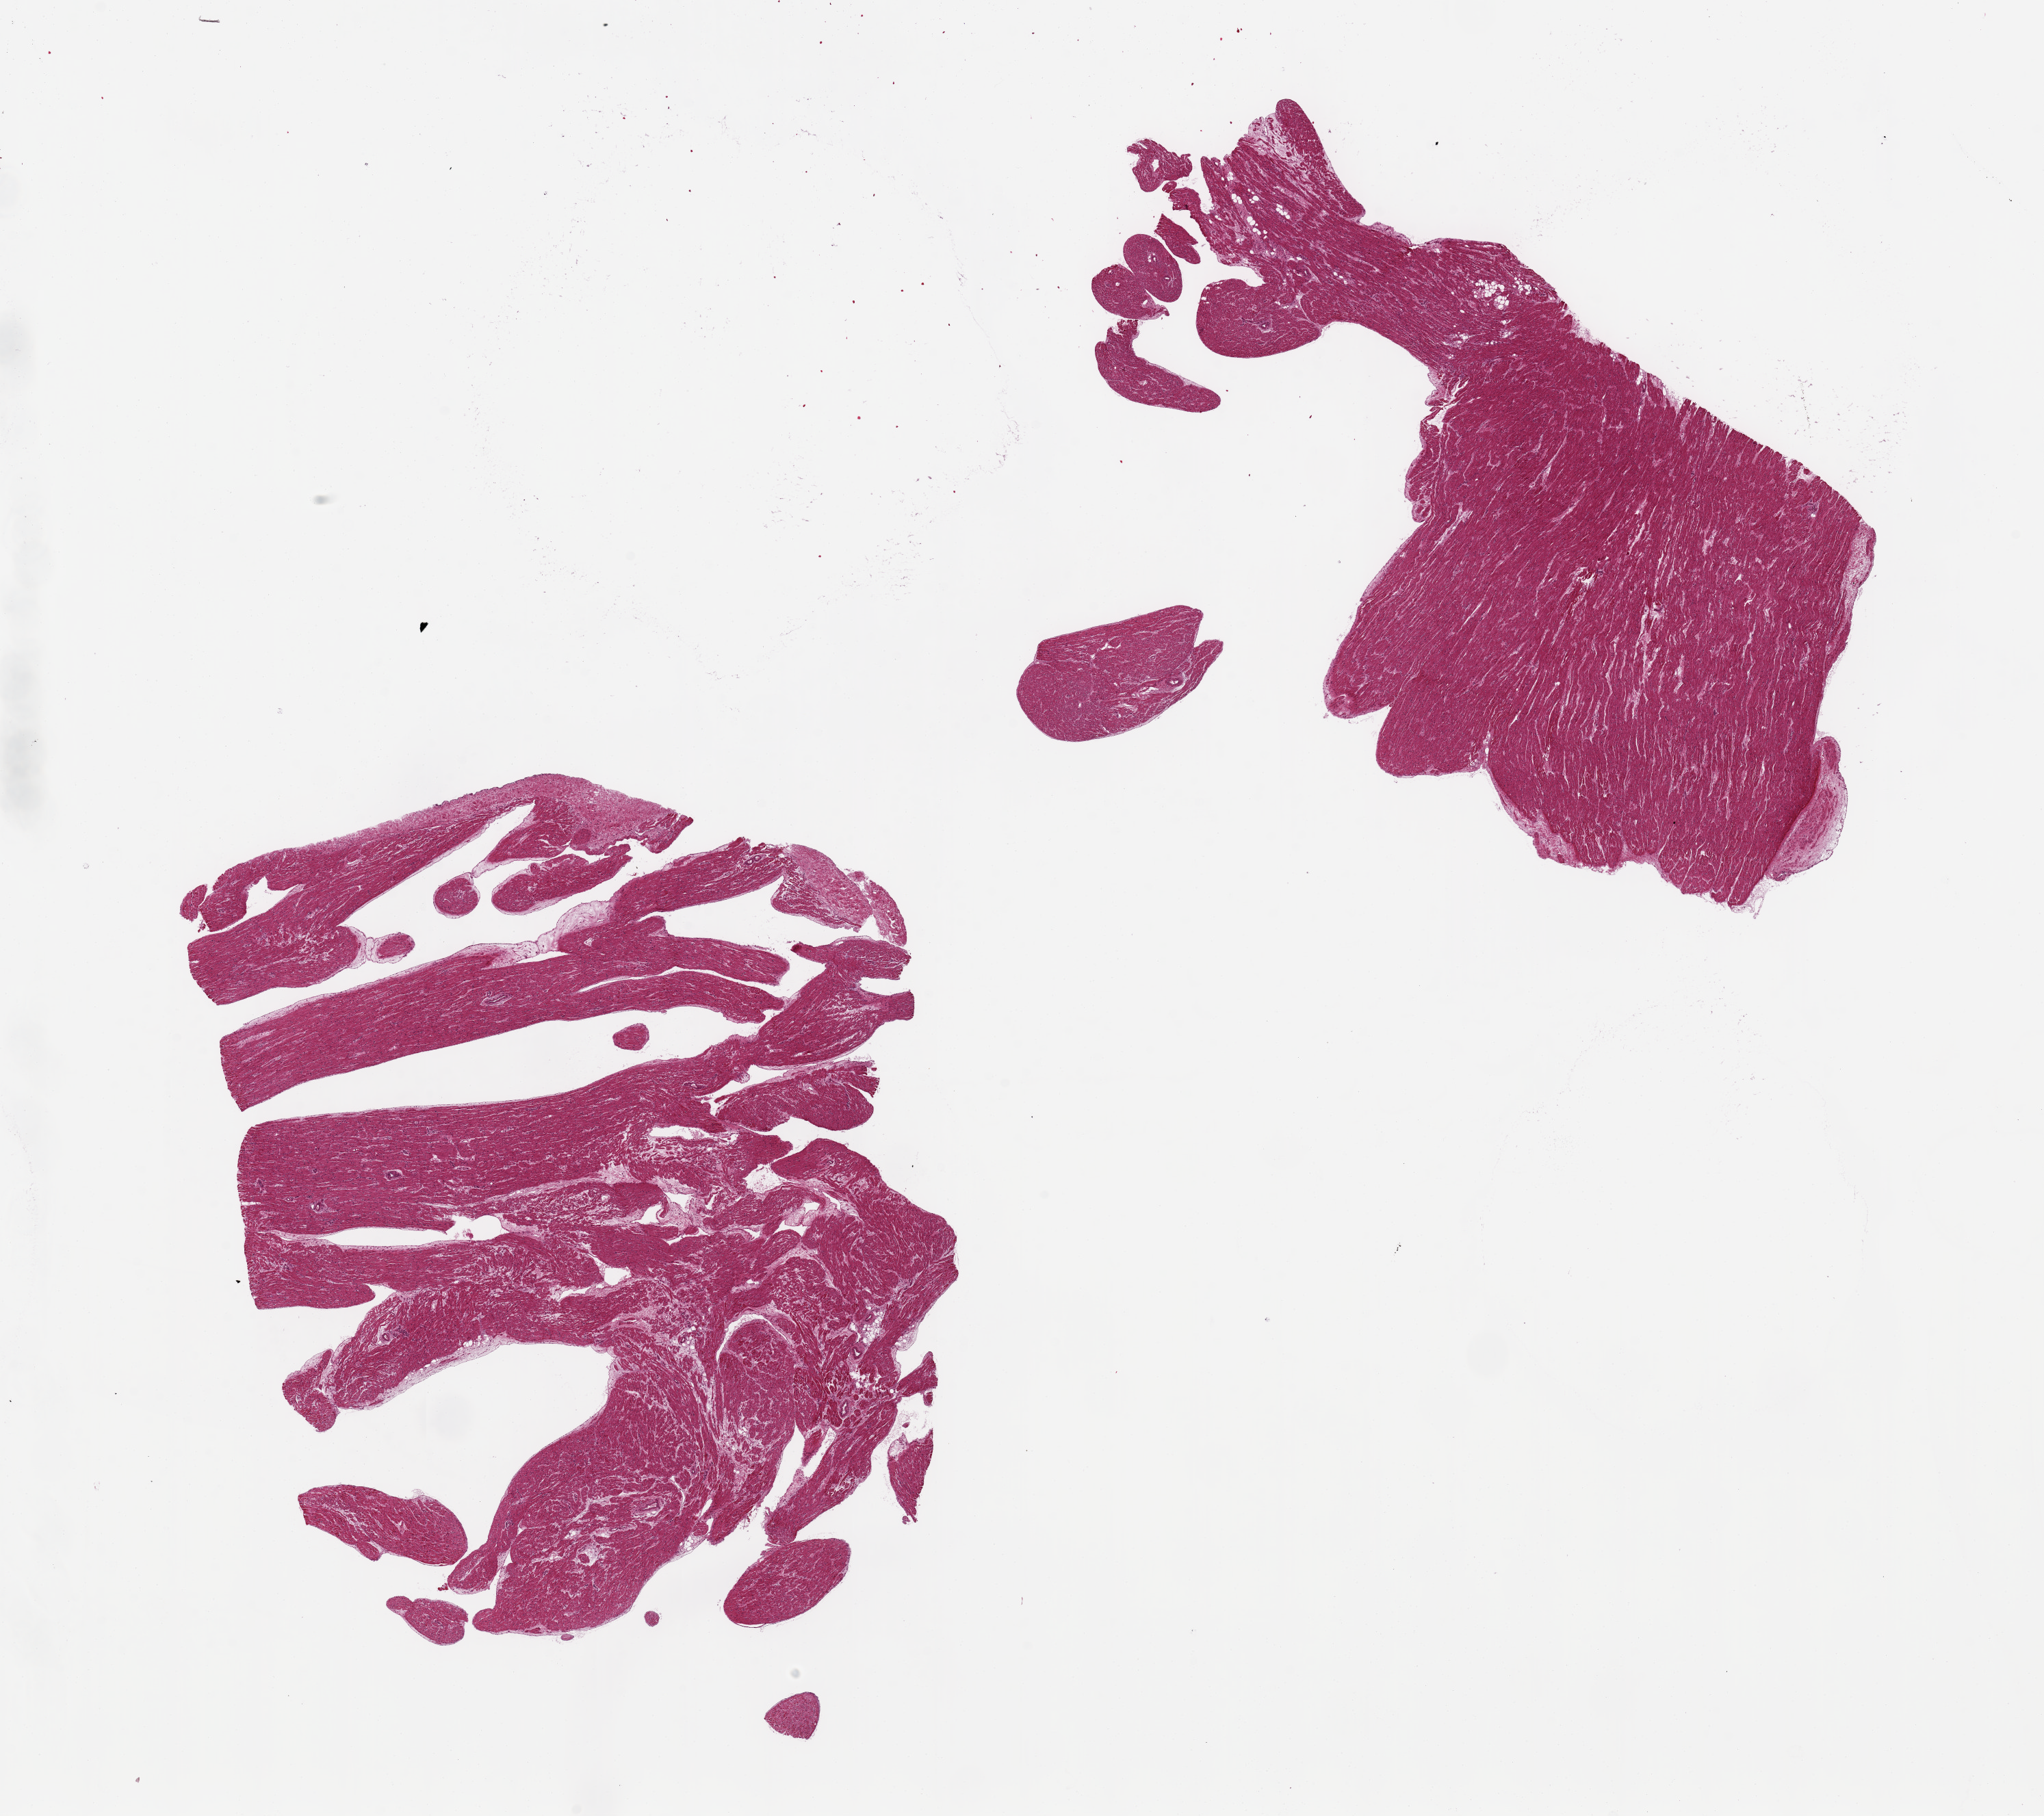
Hematoxylin and eosin (H&E) whole-slide image, brightfield — shown as a low-resolution overview of the whole scanned area (about 23.6 x 21.0 mm). PAXgene-fixed, paraffin-embedded tissue. Sampled site (target tissue): auricular appendage. Tissue donor sample. Donor: male.
• reviewer comment on this tissue sample: 2 pieces ~9x7mm